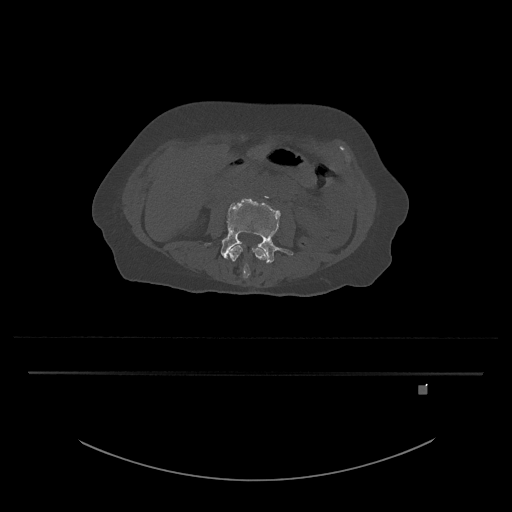
CT including the spine, one axial slice; position 386 of 797 along the scan axis; bone window (W 1800 / L 400 HU); 0.5 mm slice thickness; 512 × 512 image matrix. Patient: female, 57 years. Case-level facts recorded for this patient, not image findings: primary cancer: cervical.
Outlined on this slice (semi-automatically segmented with operator editing):
- L3 vertebra: box from (x=229, y=245) to (x=267, y=279) px
- L4 vertebra: (x=205, y=198)–(x=294, y=264)